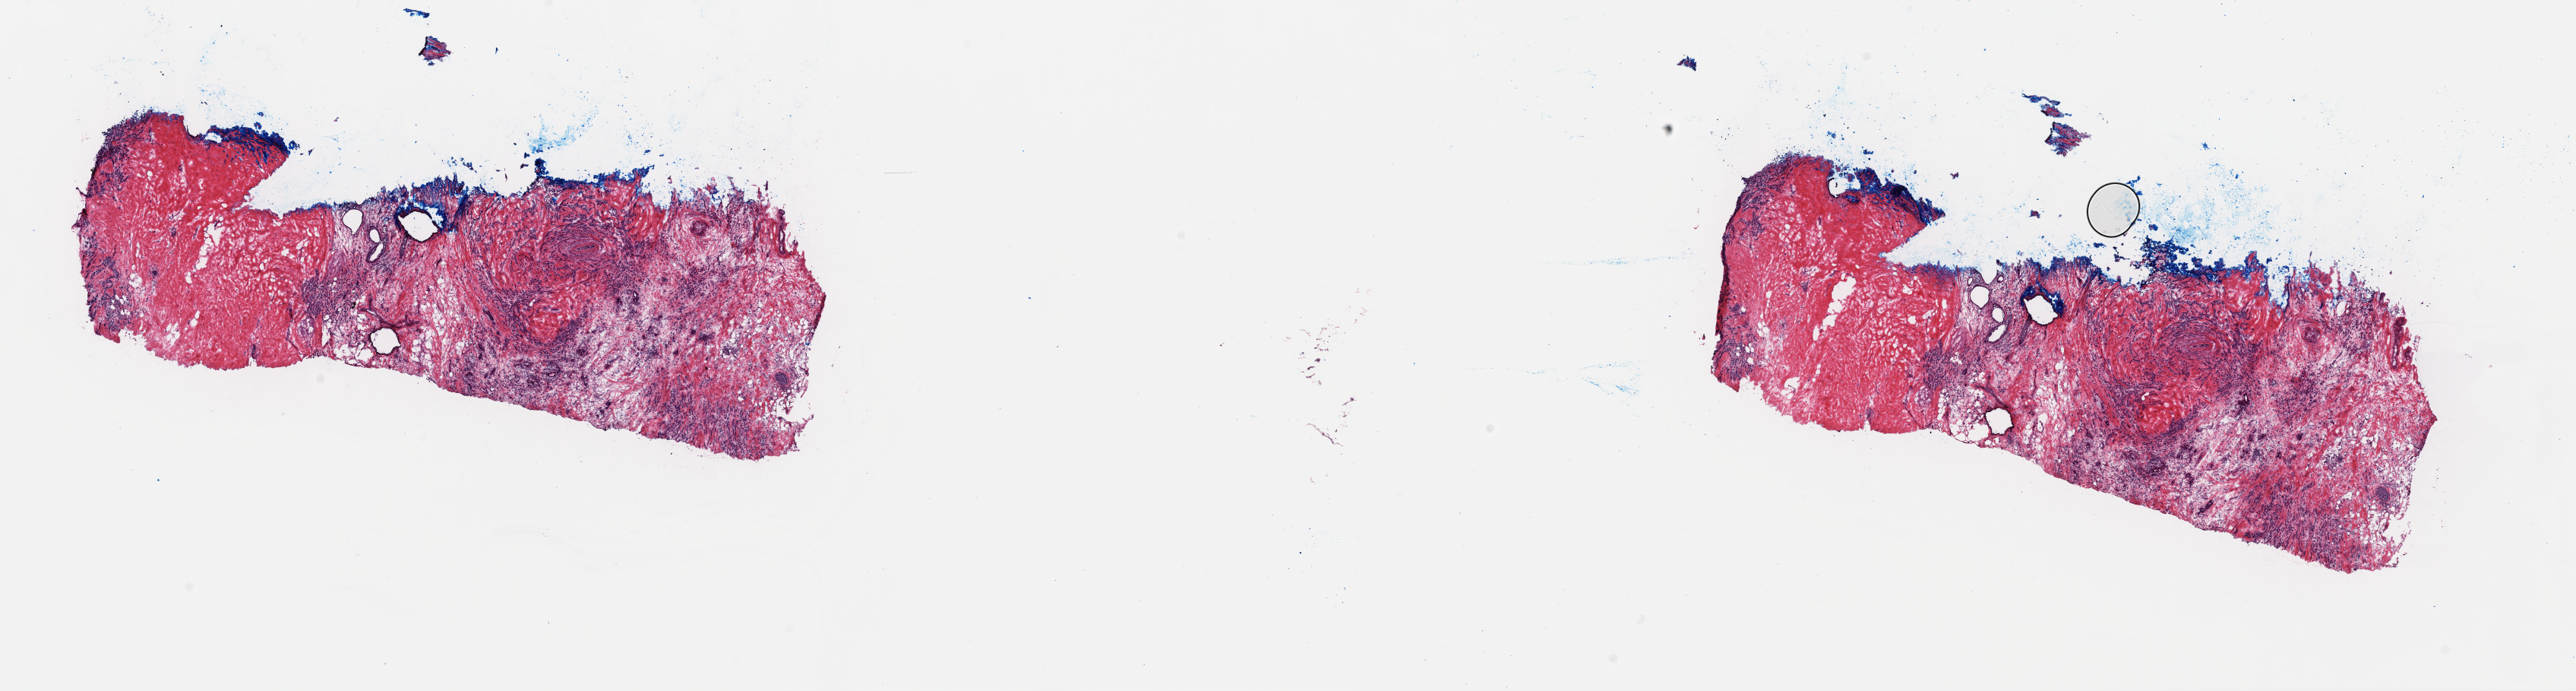
H&E whole-slide image, whole scanned area (about 26.8 x 7.2 mm) shown as a low-resolution overview; frozen section; breast, primary tumour sample. Female, age 76 years at initial diagnosis. Pathologist review of this section (percent, as recorded): tumour cells 30%, tumour nuclei 60%, normal cells 10%, stromal cells 60%, necrosis 0%. Inflammatory infiltration, as recorded: lymphocyte infiltration 0%, monocyte infiltration 0%, neutrophil infiltration 0%.
- histologic diagnosis: Lobular carcinoma, NOS
- laterality: right
- TNM: T3 N1a MX
- lymph nodes positive (case pathology): 2 of 2 examined
- AJCC pathologic stage: IIIA